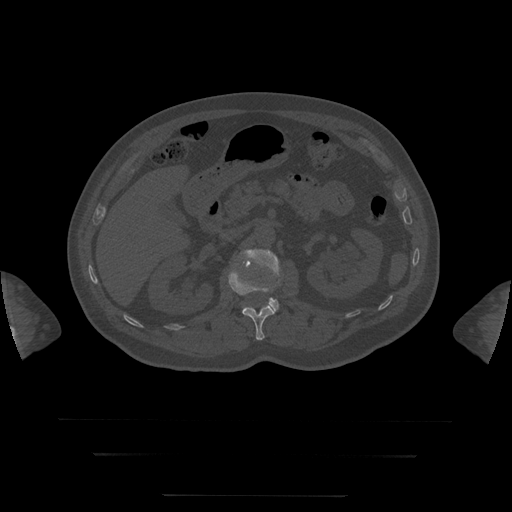
CT including the spine, one axial slice; slice 39 of 397 in the series (ordered by position); reconstruction kernel STANDARD; 120 kVp; bone window (W 1800 / L 400 HU); 1.25 mm slice thickness; 512 × 512 image matrix, field of view 510 × 510 mm. Patient age 73 years. Case-level facts recorded for this patient, not image findings: primary cancer: prostate.
Annotated regions visible in this slice (semi-automatic segmentation, software-assisted and operator-edited):
- L1 vertebra: bounding box <228,268,275,340> (left, top, right, bottom; pixels)